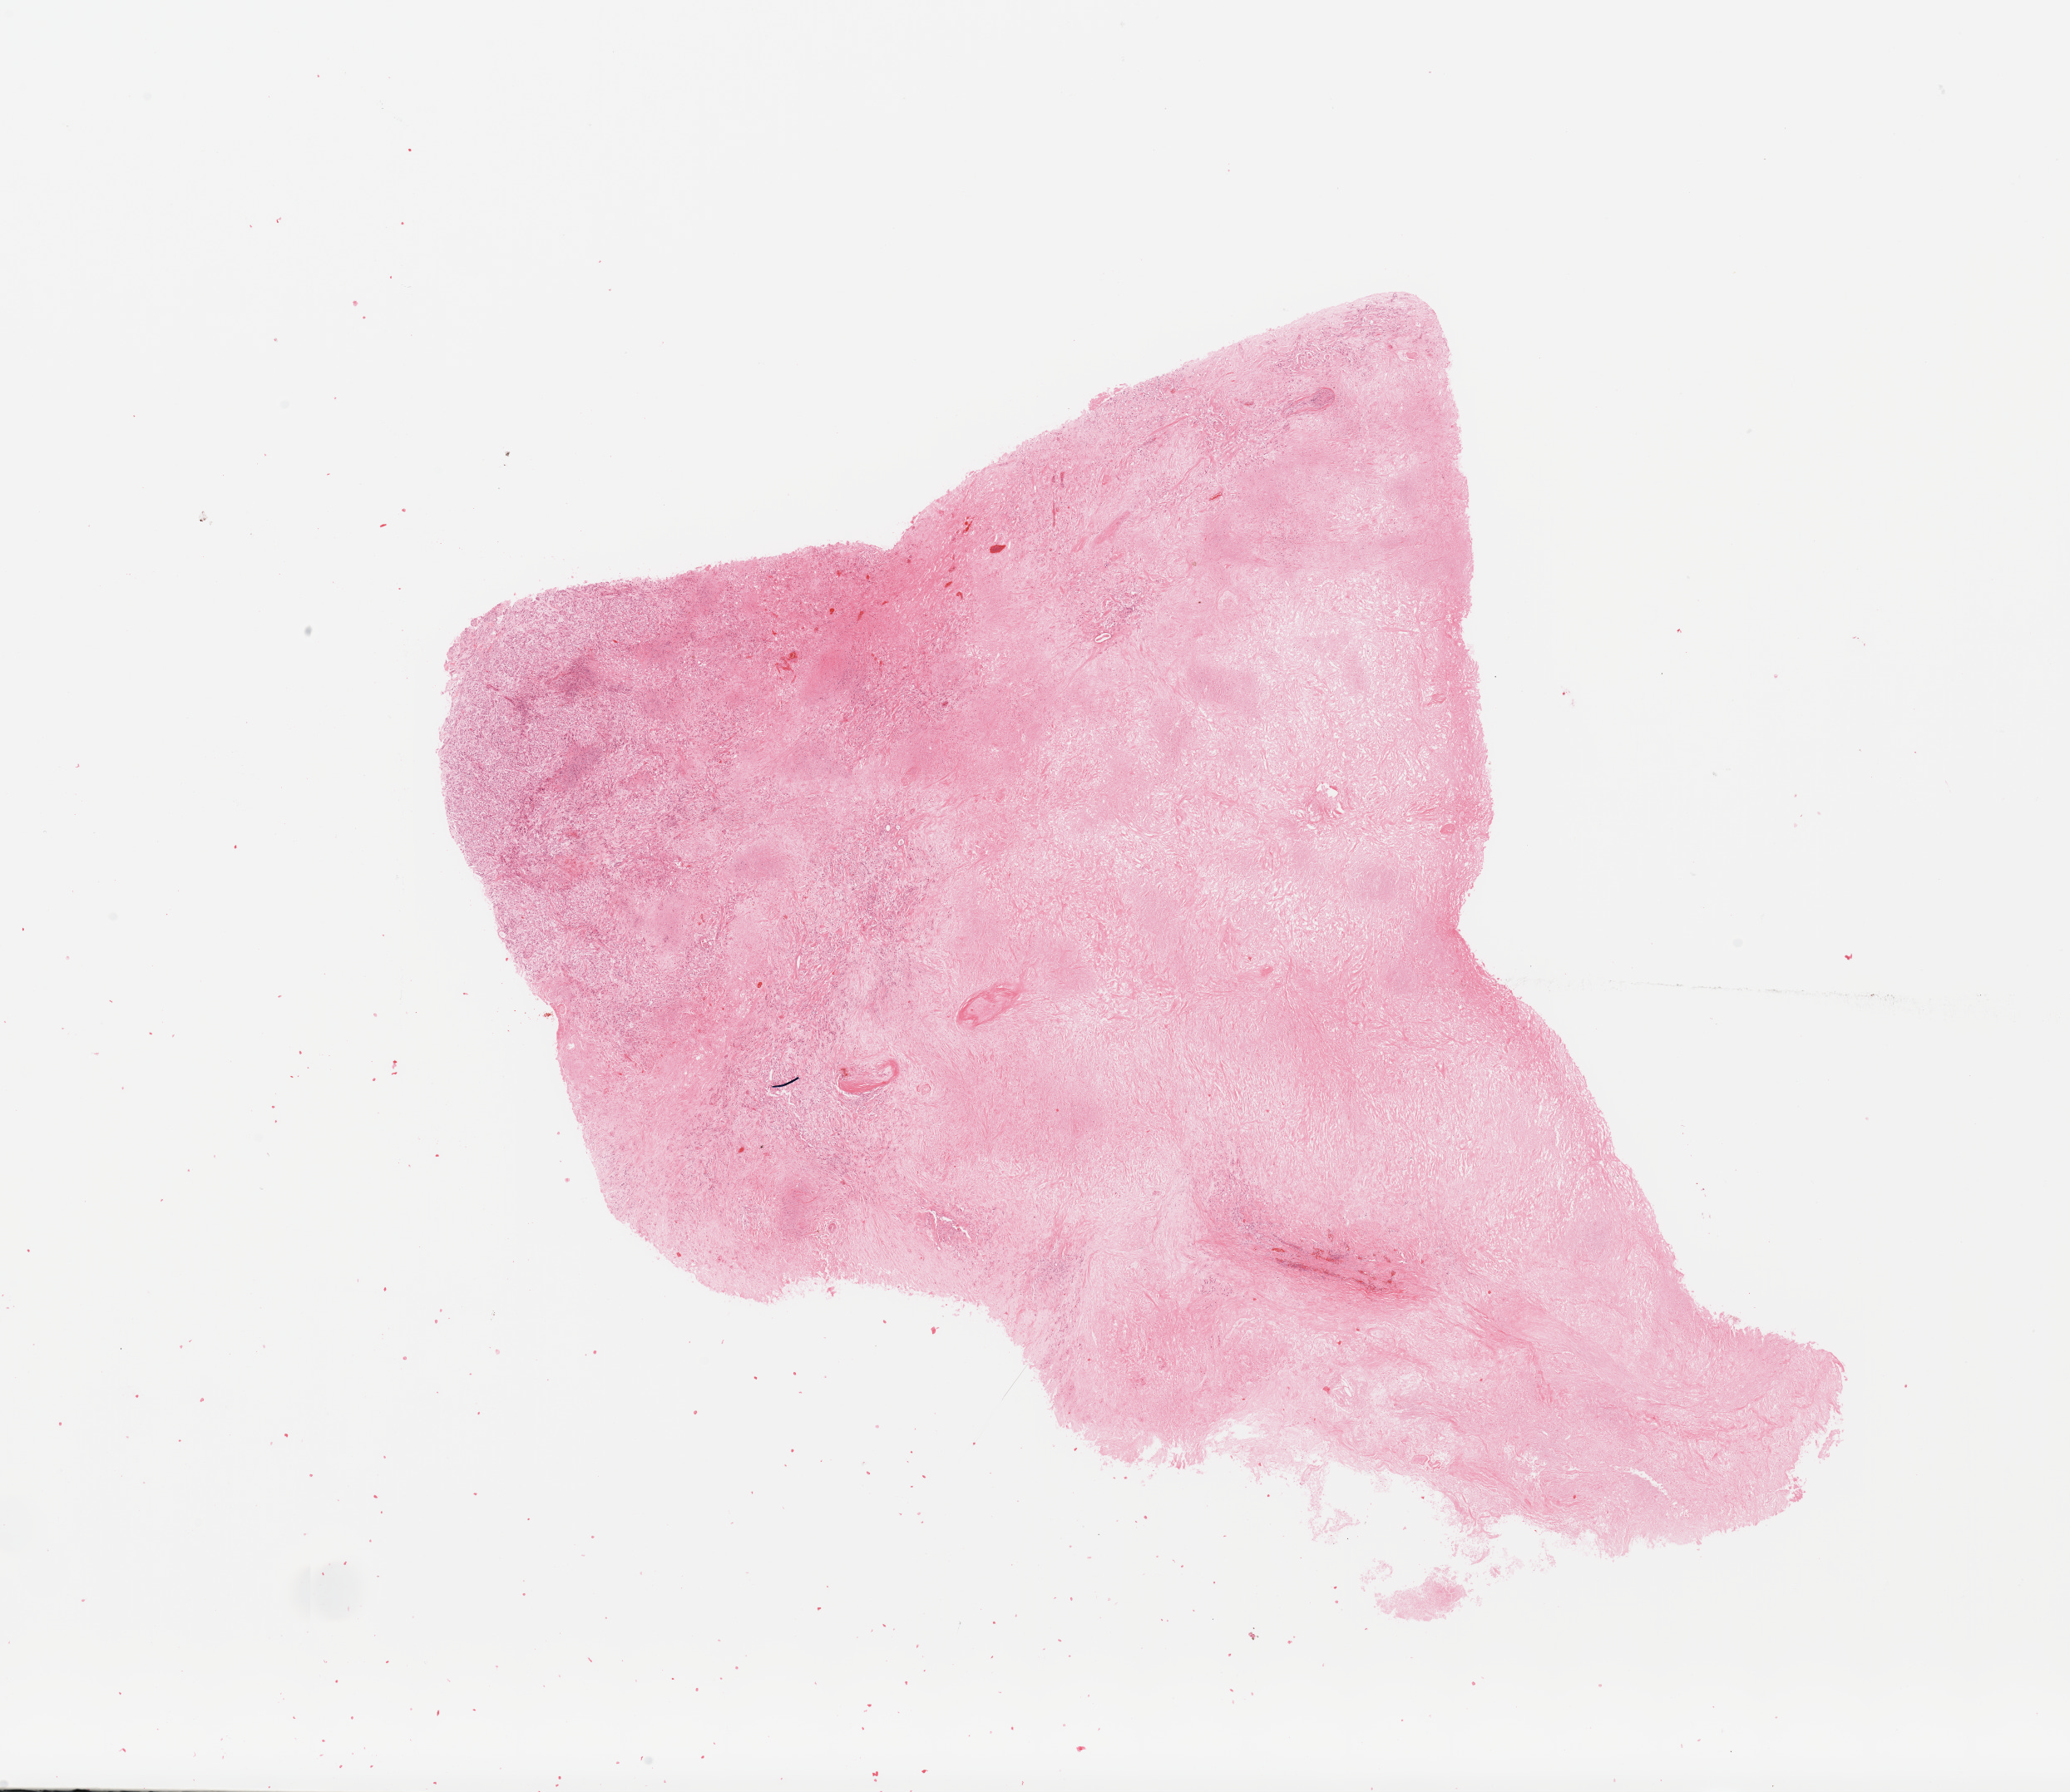
H&E-stained whole-slide image, a low-resolution overview of the entire scanned area, about 19.7 x 17.0 mm. Tumour tissue sample, sampled site: kidney. 68-year-old female patient. Histologic grade: G3 (poorly differentiated). Composition of this section per pathologist review: tumour nuclei 40%, necrosis 30%.
Diagnosis: Renal cell carcinoma, NOS. AJCC pathologic stage: IV.